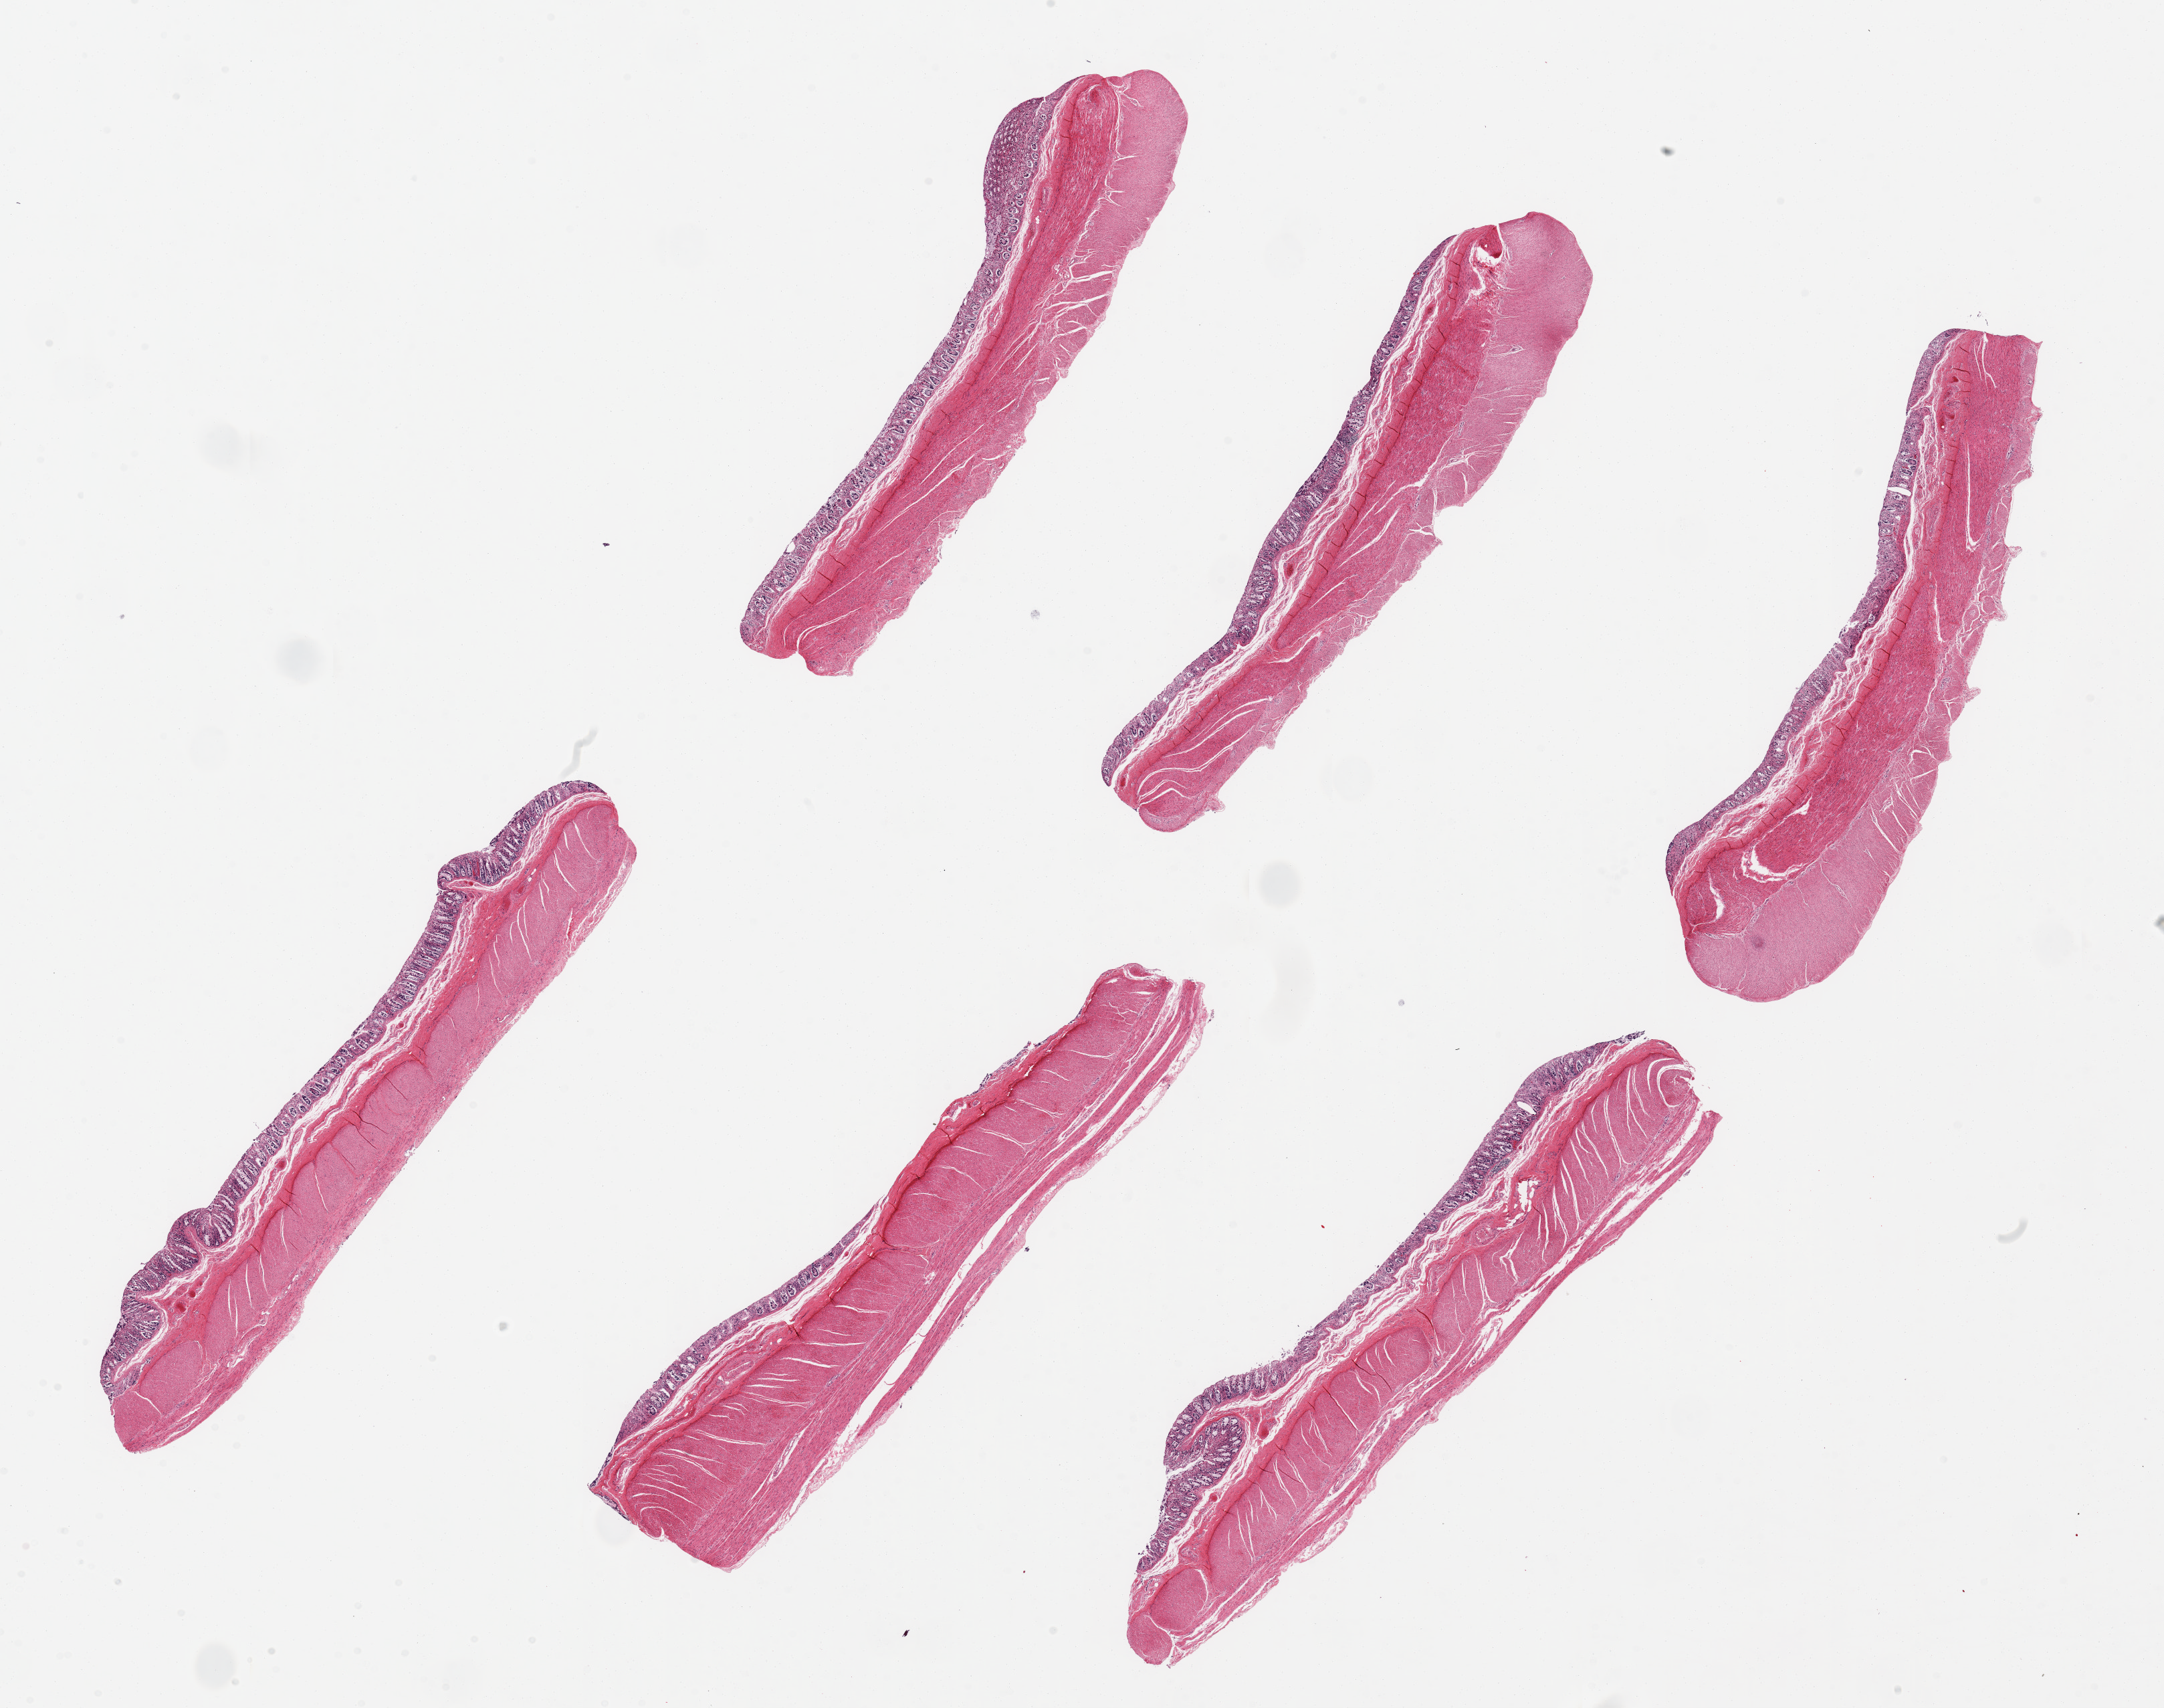
Digitized hematoxylin and eosin (H&E)-stained section, brightfield, shown as a low-resolution overview of the whole scanned area (about 25.6 x 20.2 mm, acquisition: 20x scan); PAXgene-fixed, paraffin-embedded tissue; target tissue: transverse colon; tissue donor sample. Donor sex: female.
Reviewer comment on this tissue sample: 6 ~8.5x1.5mm pieces, epithelial portions of mucosa with near total total autolysis.